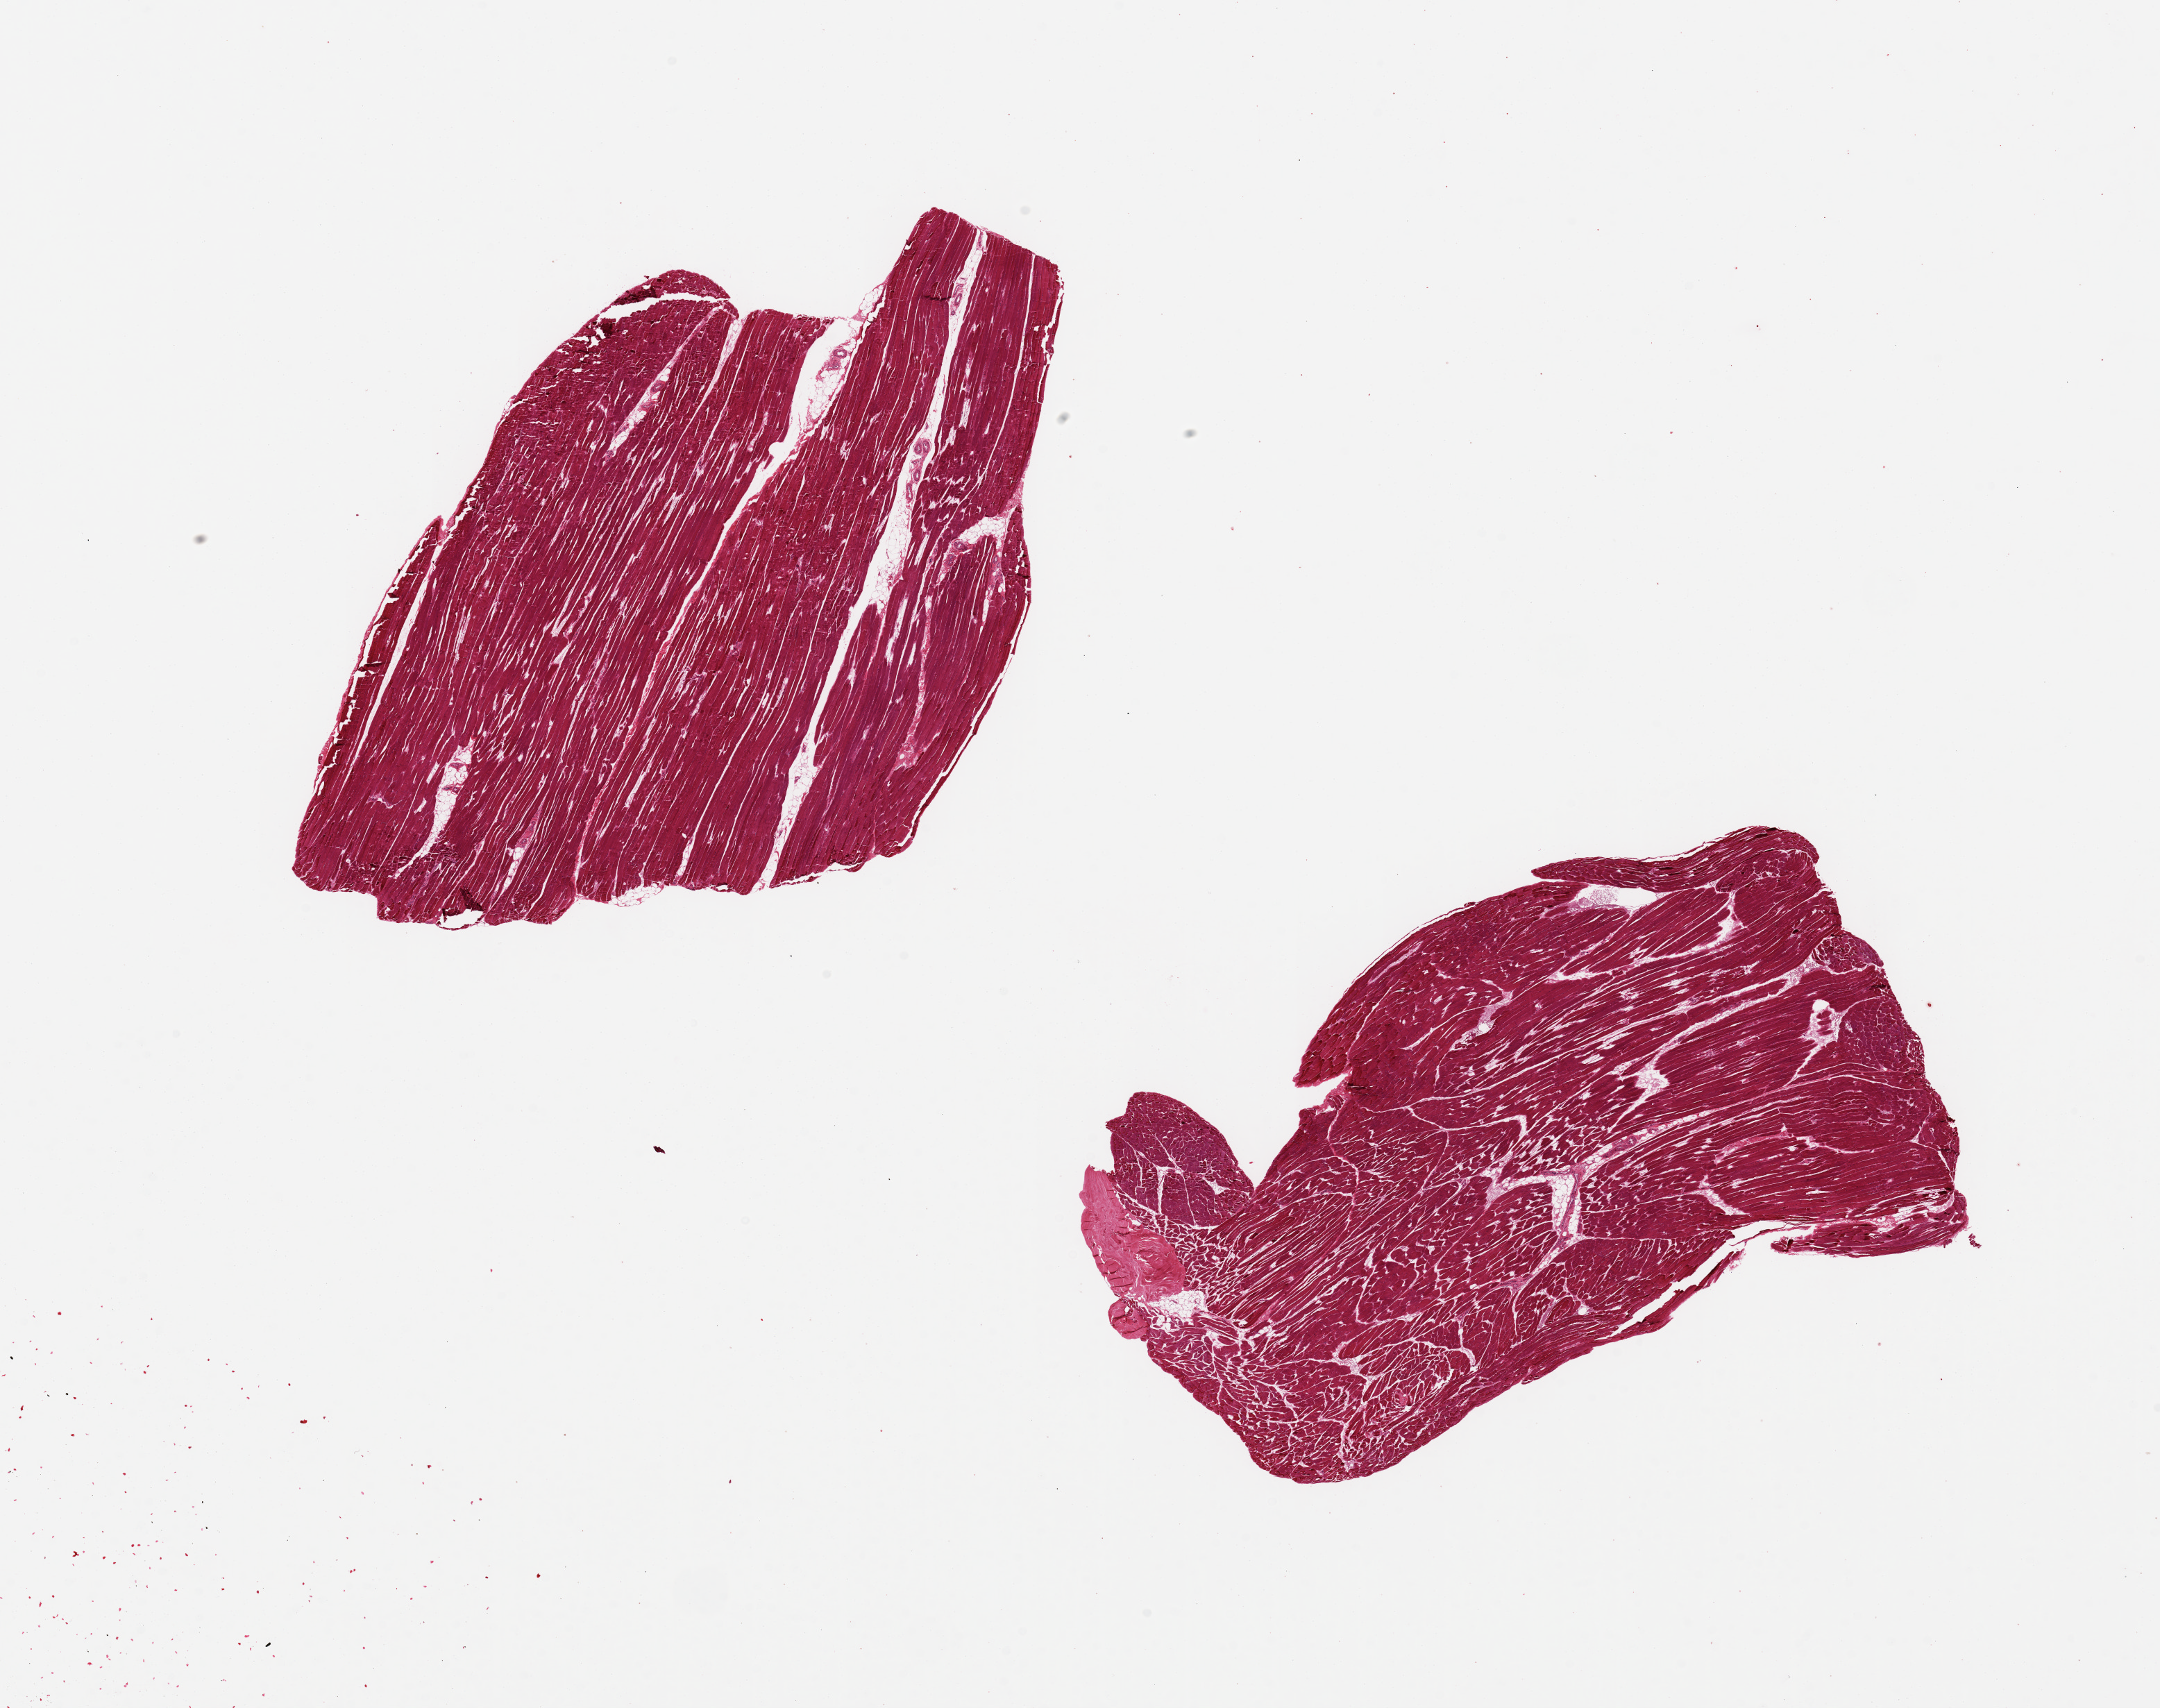
Whole-slide image, haematoxylin and eosin stain — a low-resolution overview of the entire scanned area, about 24.6 x 19.5 mm, PAXgene-fixed paraffin-embedded (PFPE) section, sampled site (target tissue): skeletal muscle, donor tissue sample. Donor sex: male.
* pathologist's review note for this sample: 2 pieces, 7x7 & 9x5mm; no extraneous adipose